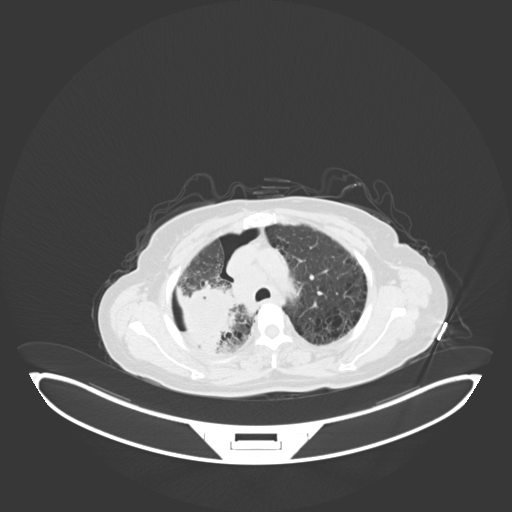
Chest CT, one axial slice. Position 46 of 69 along the scan axis. Lung window (W 1500 / L -600 HU). 3 mm slice thickness. 512 × 512 image matrix. Patient: female, 64 years. Case-level facts recorded for this patient, not image findings: clinical TNM (as recorded): T3 N3 M0.
Annotated regions visible in this slice (bounding box drawn by a radiologist):
- lung tumour (recorded histology: squamous cell carcinoma): bounding box [x1, y1, x2, y2] px = [167, 281, 239, 355]